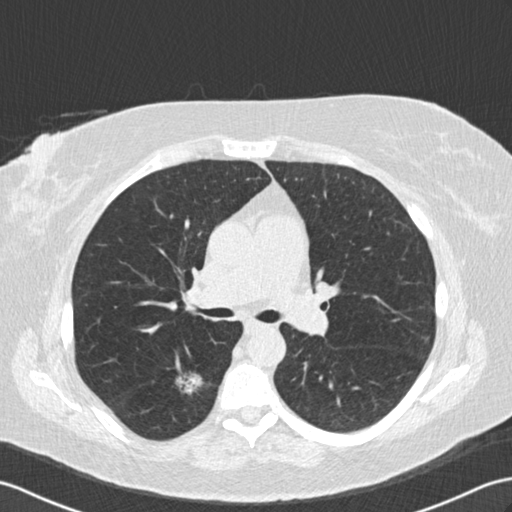
Low-dose screening chest CT, one axial slice; lung window (W 1500 / L -600 HU); 2 mm slice thickness; 512 × 512 image matrix, field of view 352 × 352 mm.
Annotated regions visible in this slice (outlined manually by an expert reader):
- lesion 1 (tumor, lower lobe of right lung): box from (x=176, y=371) to (x=203, y=395) px